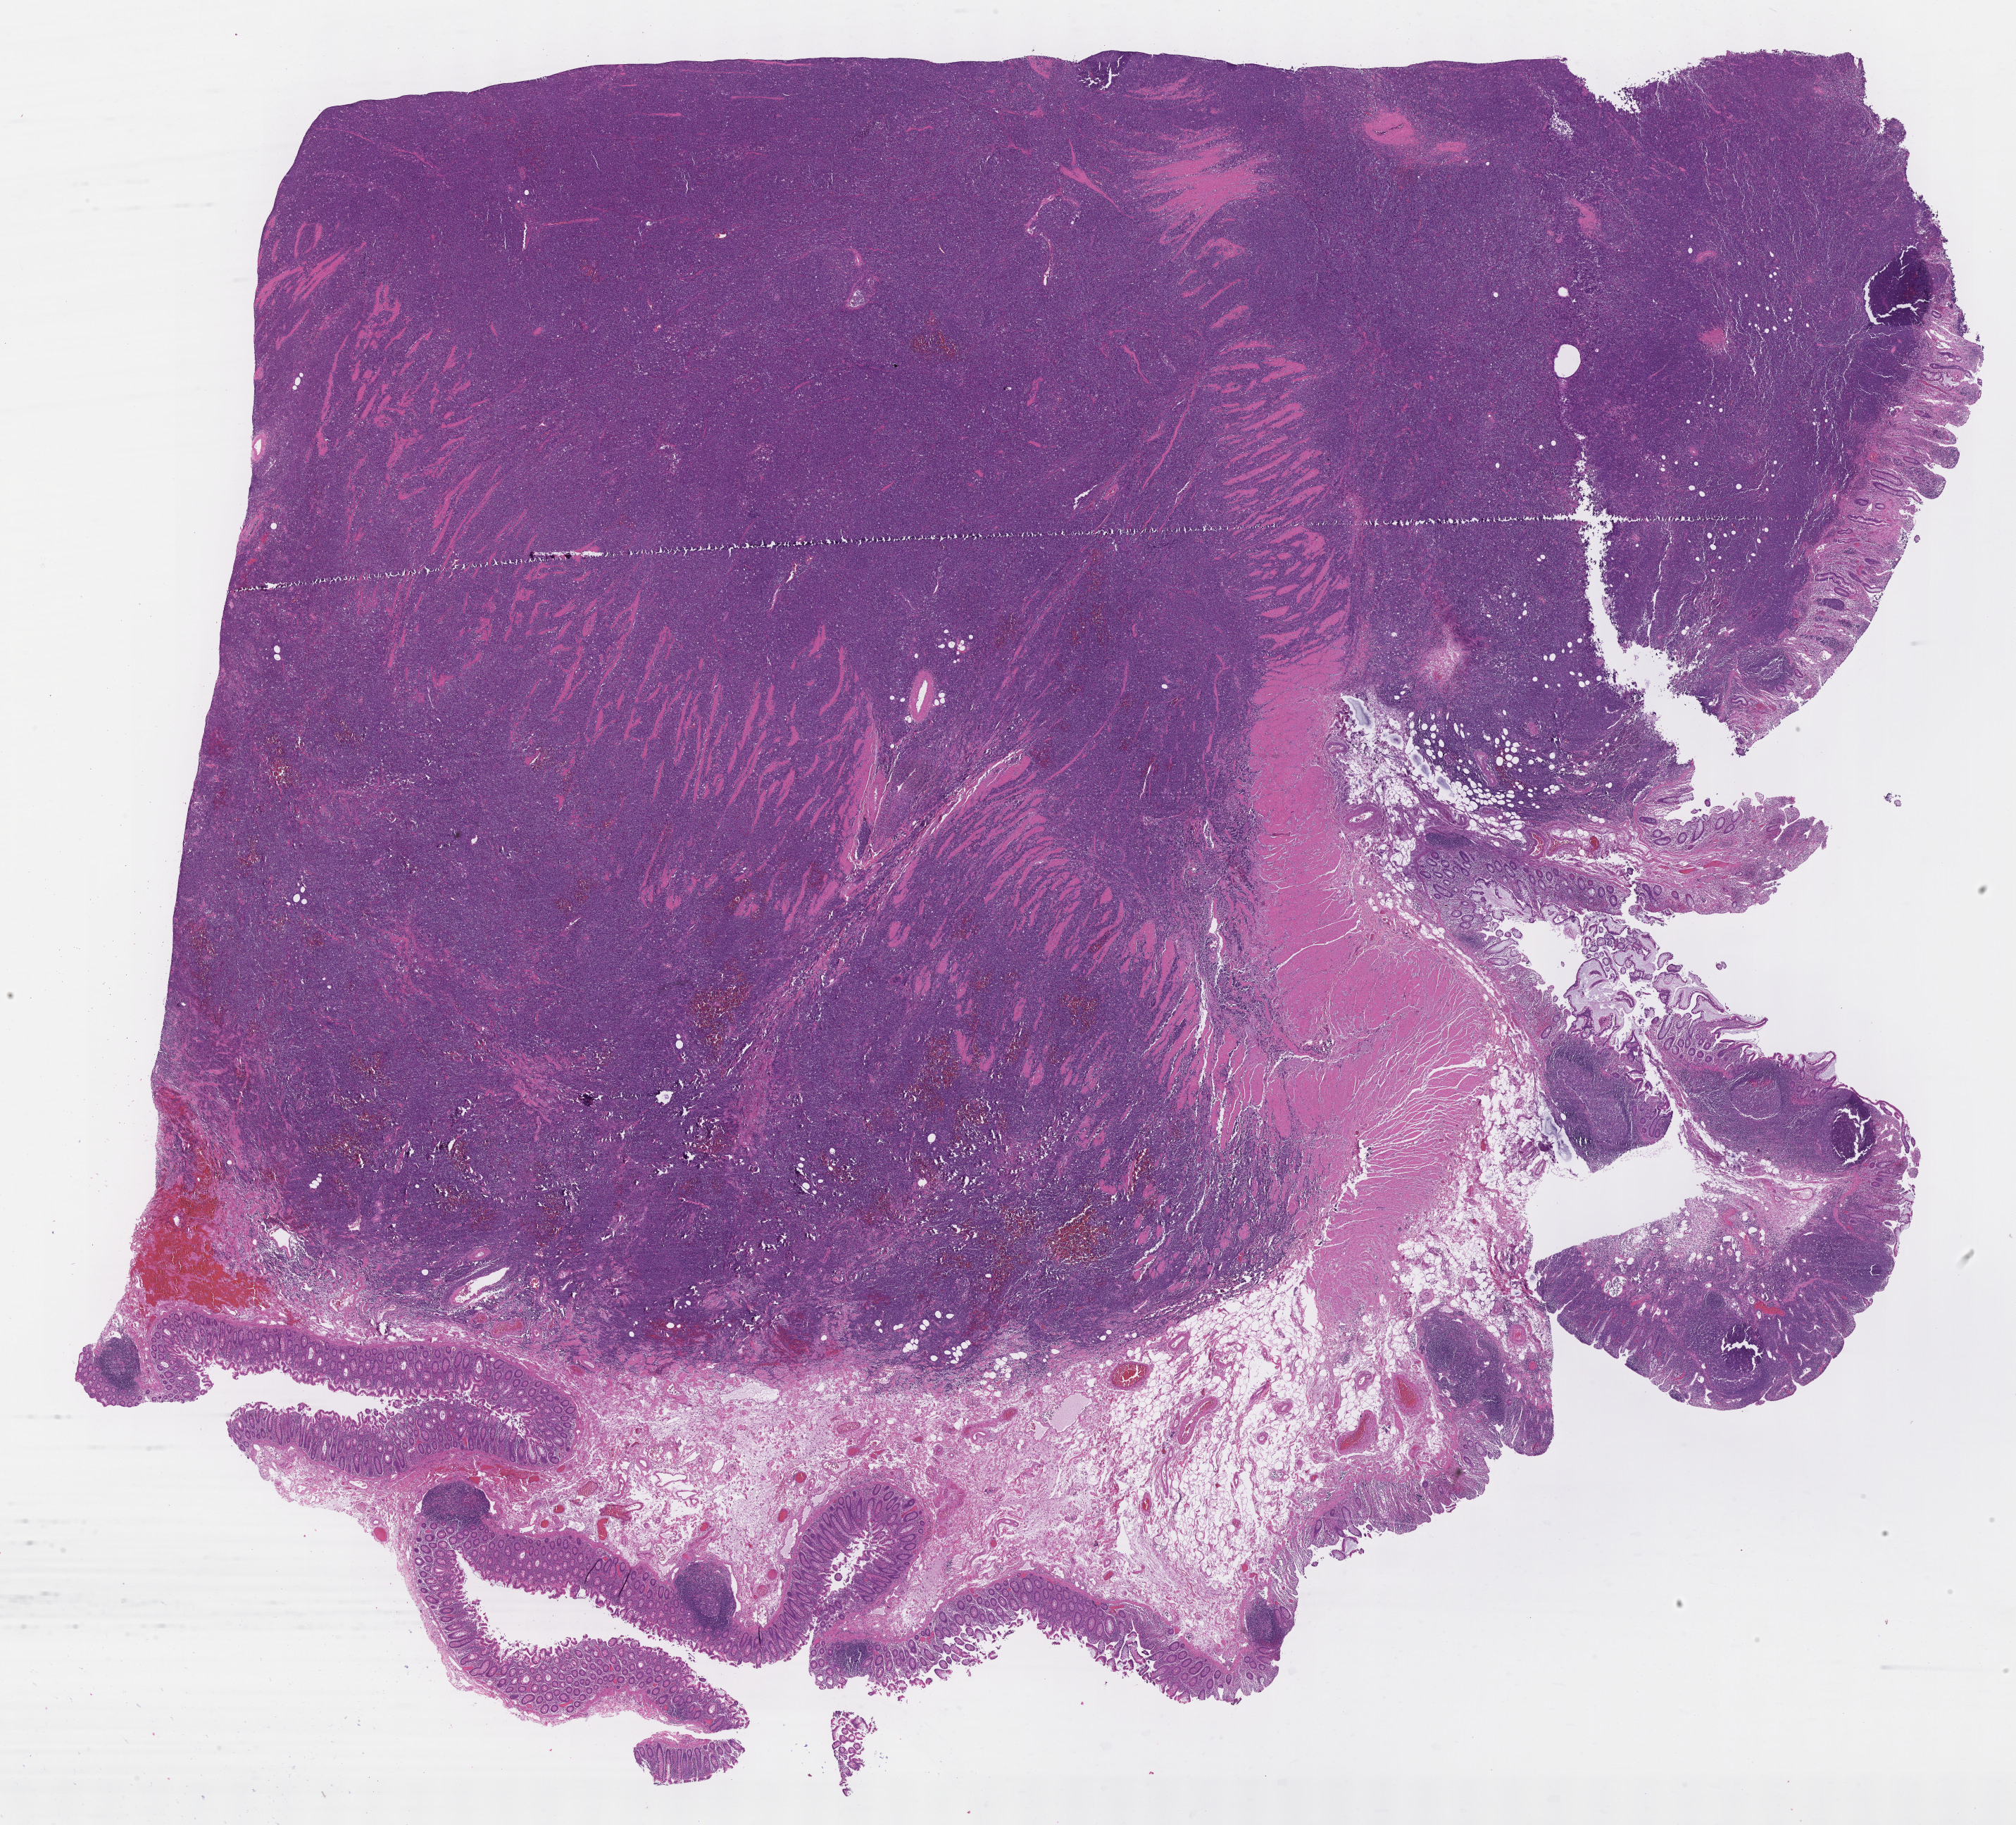
Whole-slide image, haematoxylin and eosin stain — low-resolution overview of the scanned area, about 23.1 x 21.0 mm, specimen: tumor tissue. Patient male; age 59 years.
• diagnosis: Burkitt lymphoma, NOS